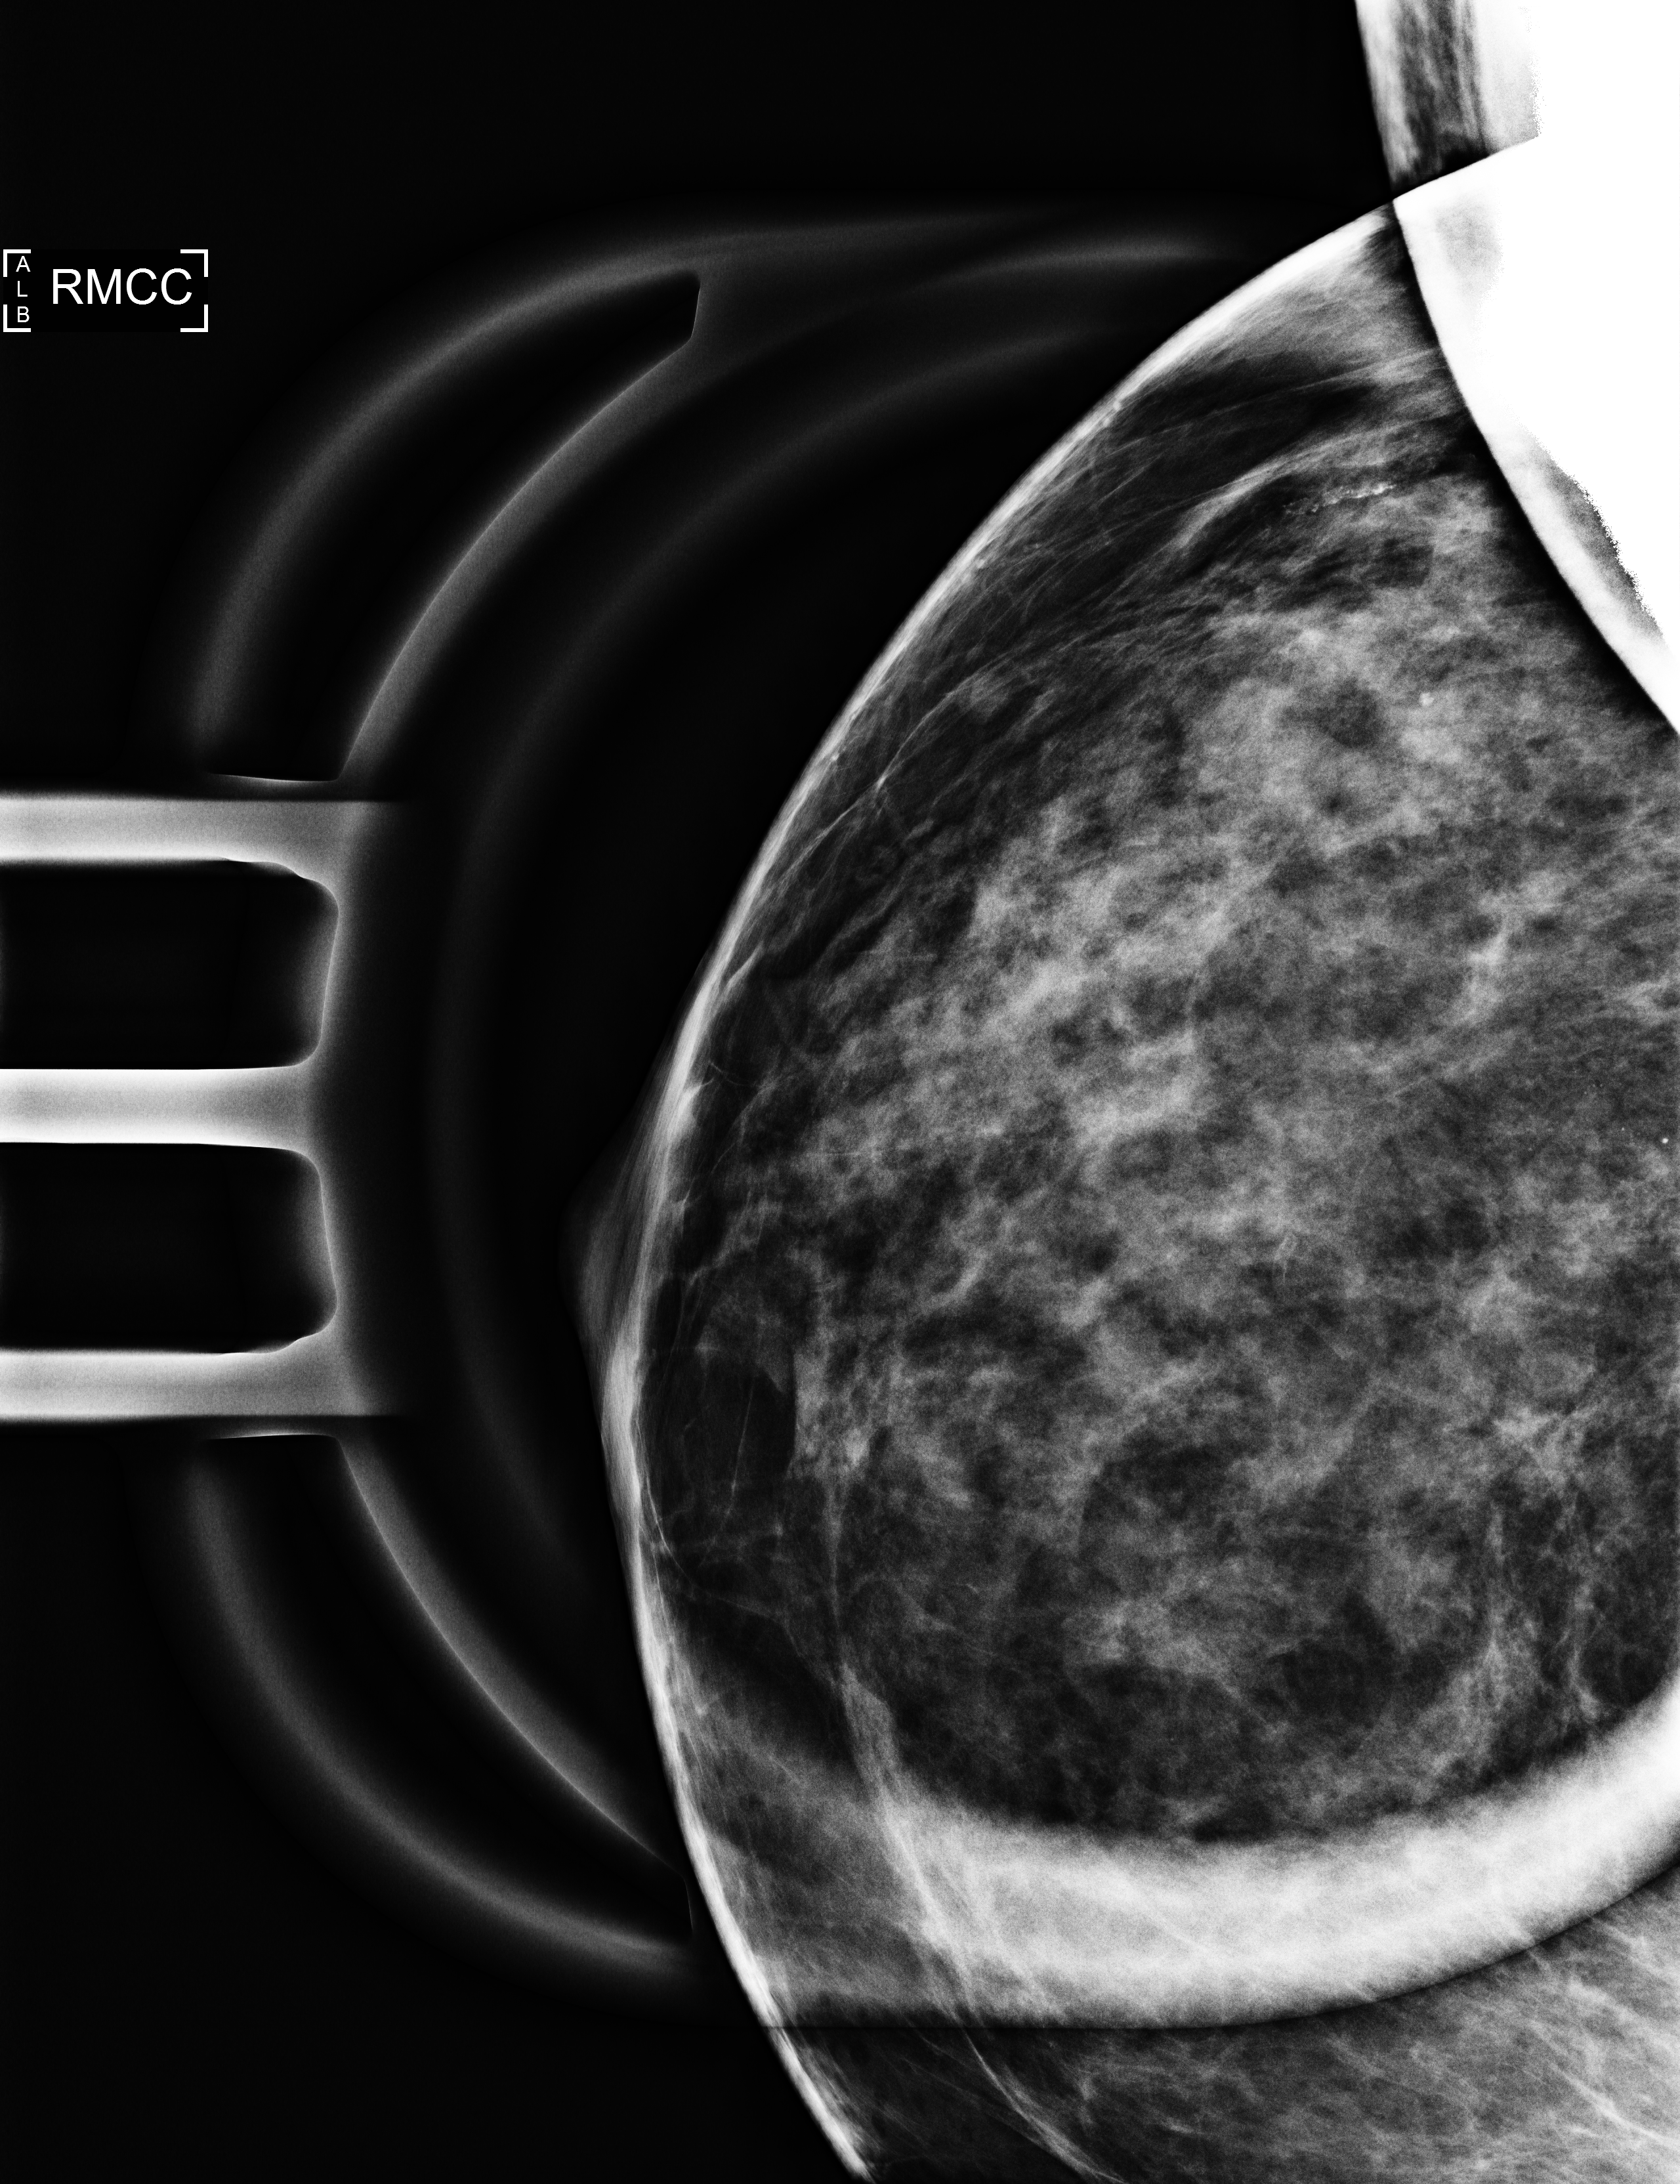
Additional work-up view; compressed breast thickness 46 mm; system: Selenia Dimensions. Female patient, age 55 years.
Image type: full-field digital mammogram. Breast: right. Projection: cranio-caudal projection, magnification.